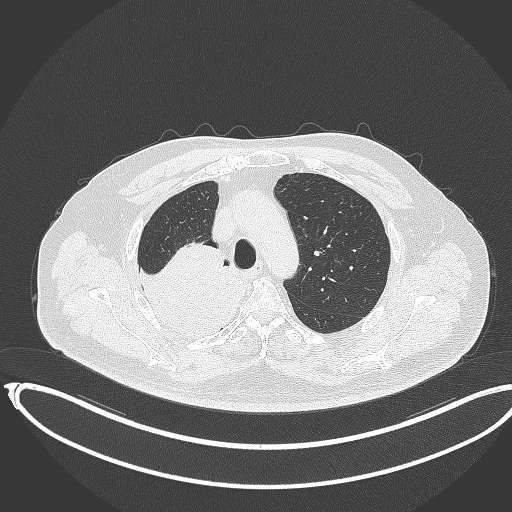
Chest CT, one axial slice. Slice 278 of 403 in the series (ordered by position). Reconstruction kernel B70f. 120 kVp. Lung window (W 1500 / L -600 HU). 1 mm slice thickness. 512 × 512 image matrix, field of view 436 × 436 mm. Patient: male, 68 years. From the clinical record (not read from this slice): clinical TNM (as recorded): T2a N0 M0.
Structures marked on this image (rectangle marked by the reading radiologist):
- lung tumour (recorded histology: adenocarcinoma): bounding box (x1, y1, x2, y2) in pixels: (132, 237, 250, 344)